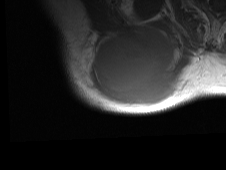
MRI of an extremity soft-tissue mass, one axial slice. Slice 54 of 81 in the series (ordered by position). MR volume resampled by the dataset authors to the PET/CT grid (not the native acquisition matrix). 3.27 mm slice thickness. 226 × 170 image matrix, field of view 221 × 166 mm. Male patient. From the clinical record (not read from this slice): histological type: pleiomorphic spindle cell undifferentiated; grade: high; site of the primary tumour: right parascapusular.
Outlined on this slice (expert contour drawn on MRI and transferred to this co-registered scan by the dataset authors):
- gross tumour volume including surrounding oedema: bounding box <74,26,193,109> (left, top, right, bottom; pixels)
- gross tumour volume (mass): <94,31,175,107>